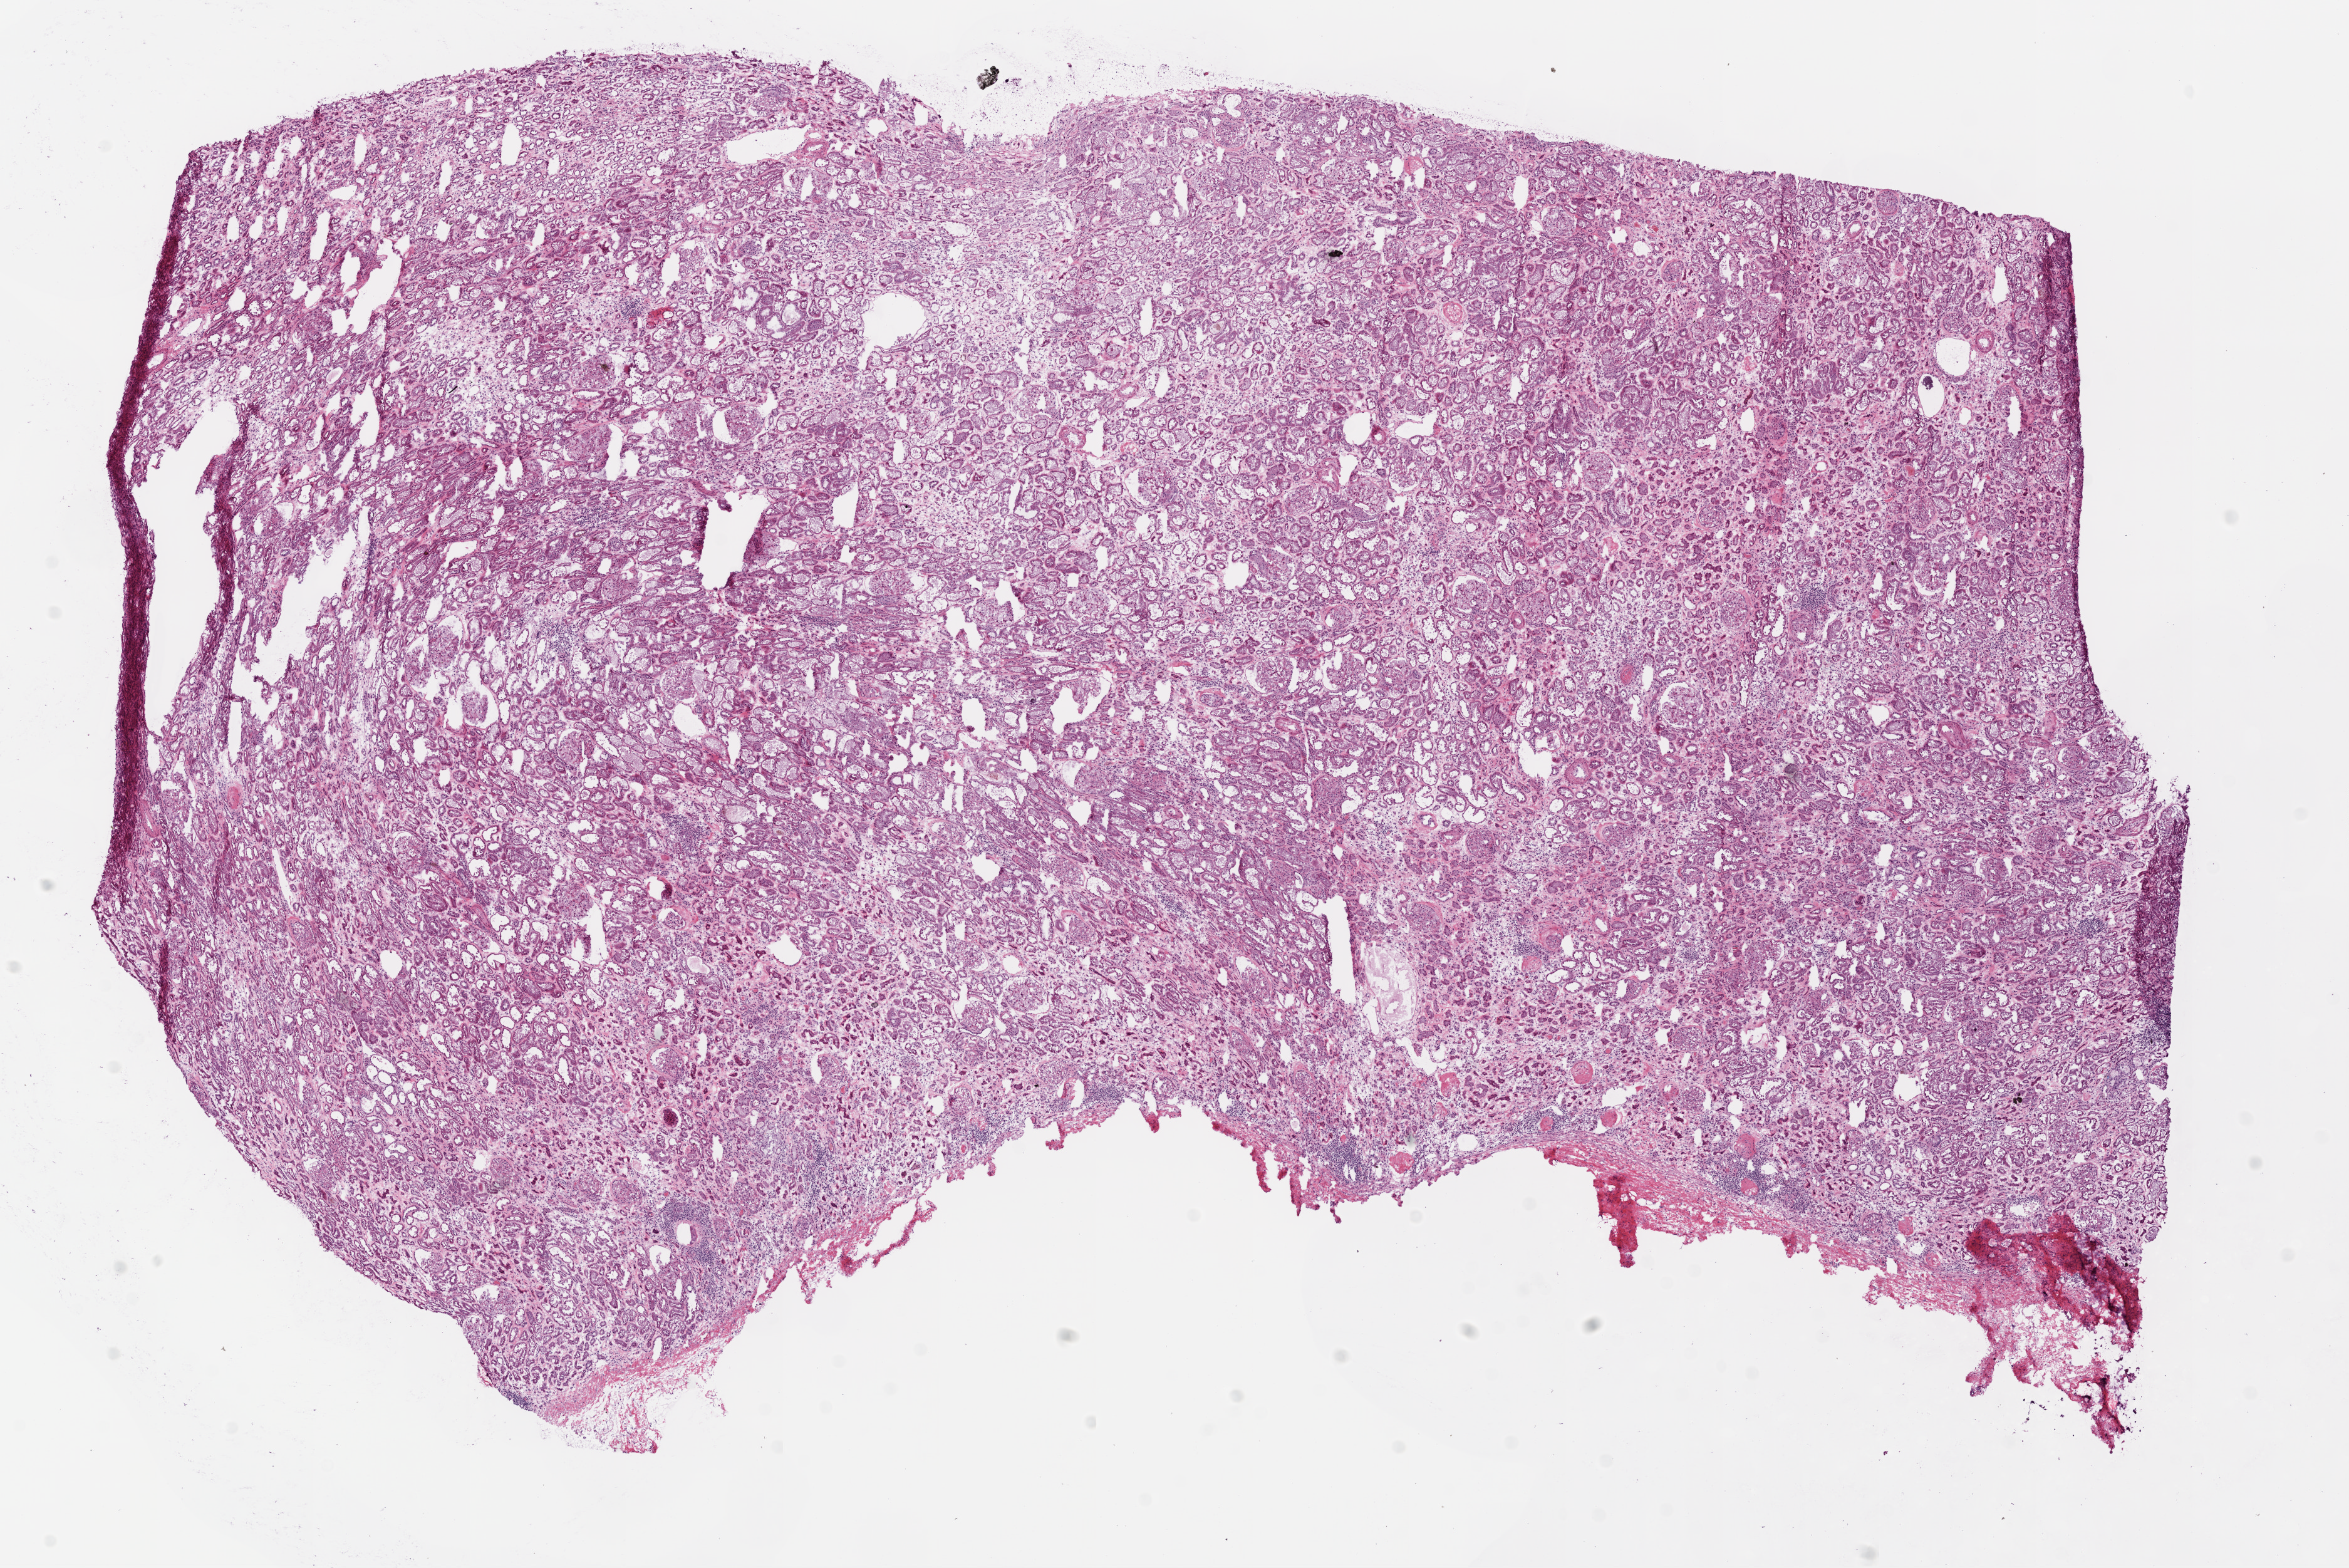
Whole-slide histology image, H&E — whole scanned area (about 15.0 x 10.0 mm) shown as a low-resolution overview, frozen section from the bottom of the tissue portion, solid tissue normal (non-tumour tissue) sample from the kidney. Male patient; age at initial diagnosis 56 years.
* this section: solid tissue normal (non-tumour) sample from the same patient
* patient diagnosis: Papillary adenocarcinoma, NOS